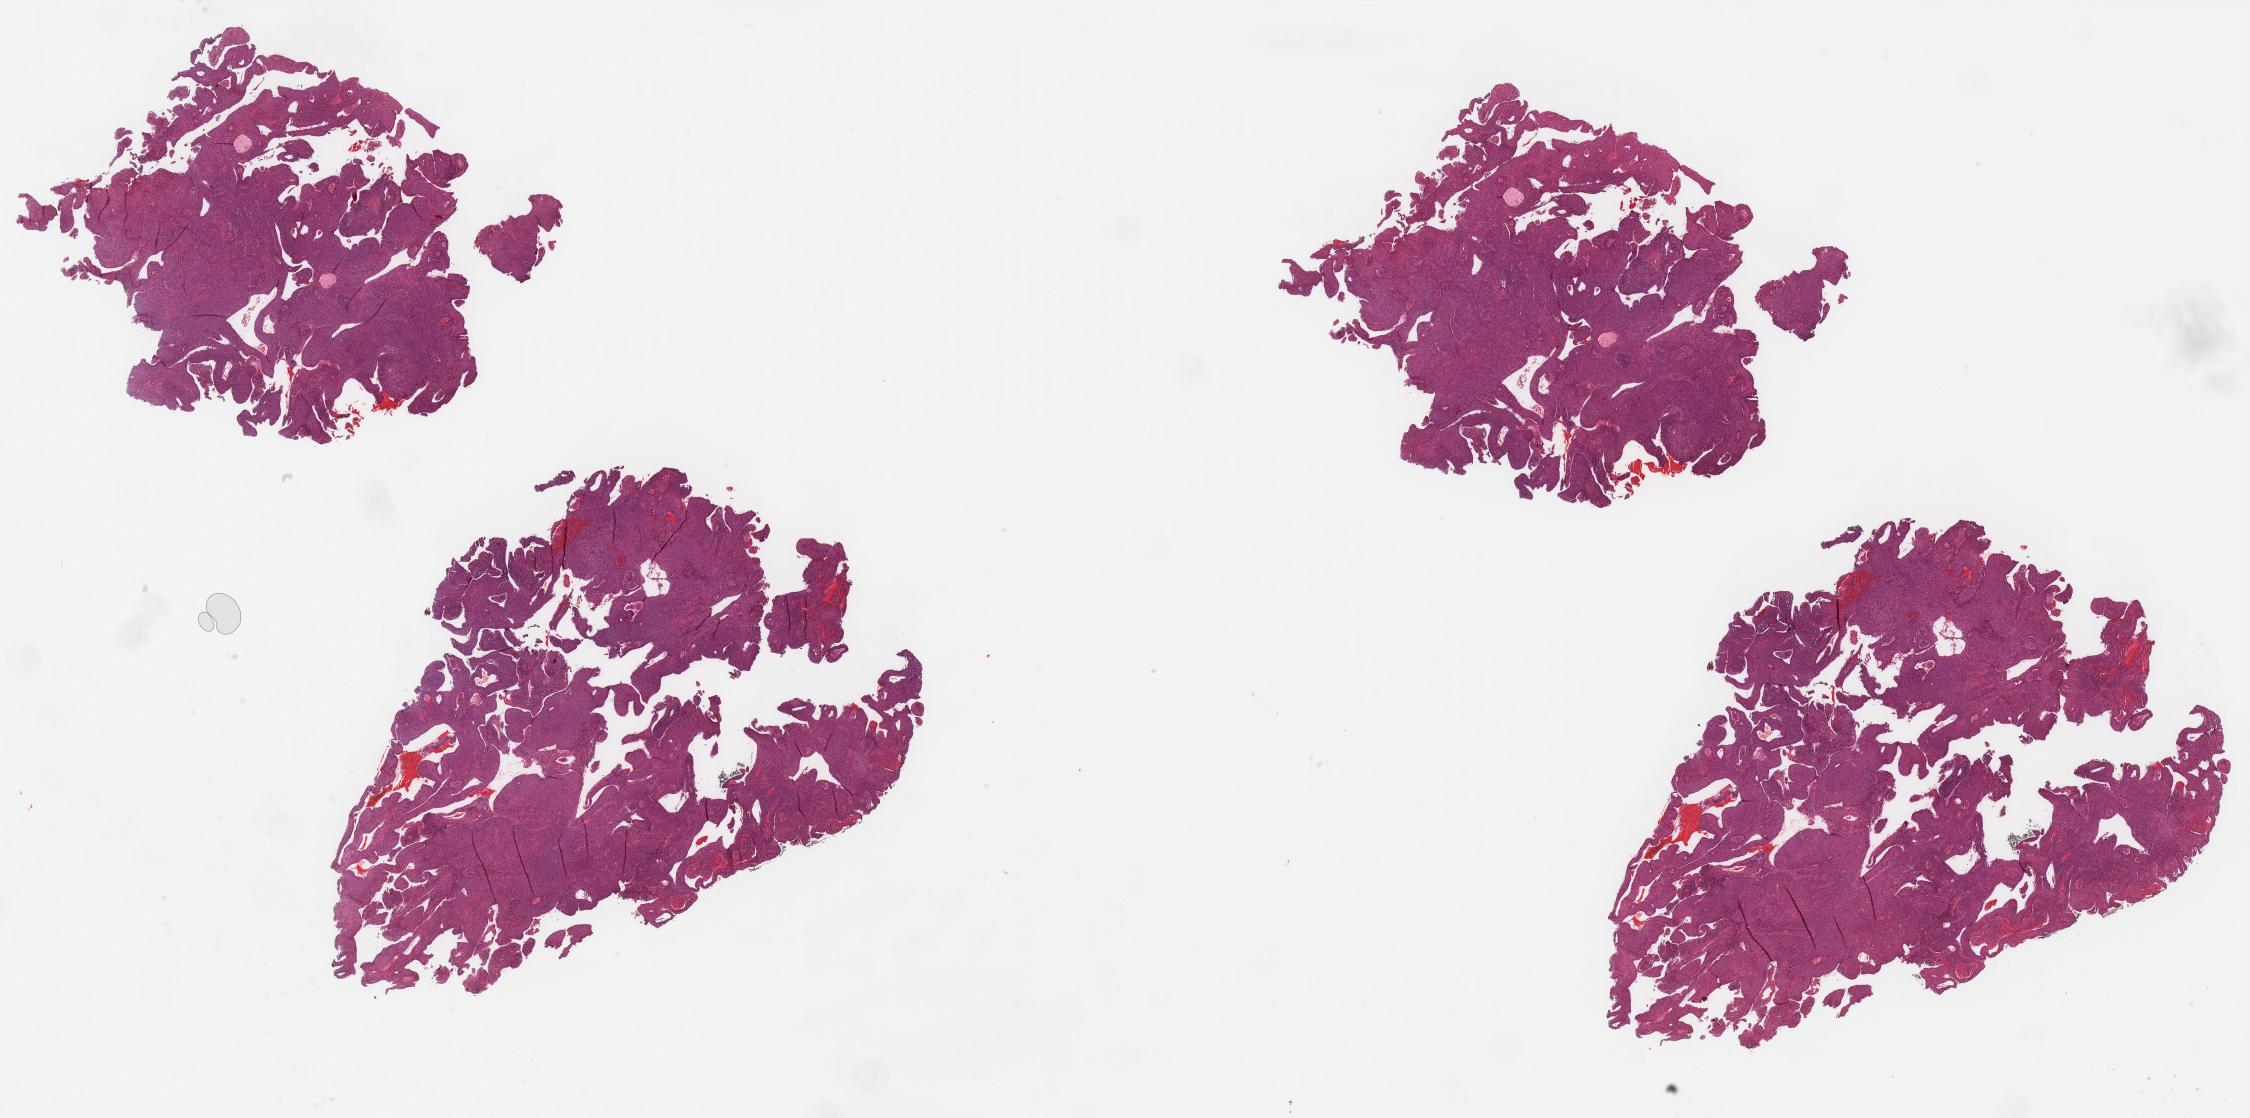
Digitized H&E tissue section (whole slide) — low-resolution overview of the scanned area, about 36.0 x 17.9 mm (slide scanned at 40x). FFPE section. Cervix, primary tumour sample. Female patient; age at initial diagnosis 30 years. Histologic grade: G2 (moderately differentiated).
• lymph nodes positive (case pathology): 0 of 8 examined
• diagnosis: Squamous cell carcinoma, NOS (cervix uteri)
• FIGO stage: IB1